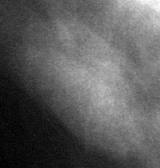
Crop from a digitized film mammogram around one marked abnormality, right breast, CC view.
Mass, shape oval, margins circumscribed; BI-RADS assessment category 3; subtlety rating 5 on a 1 (subtle) to 5 (obvious) scale; pathology (as recorded): benign.